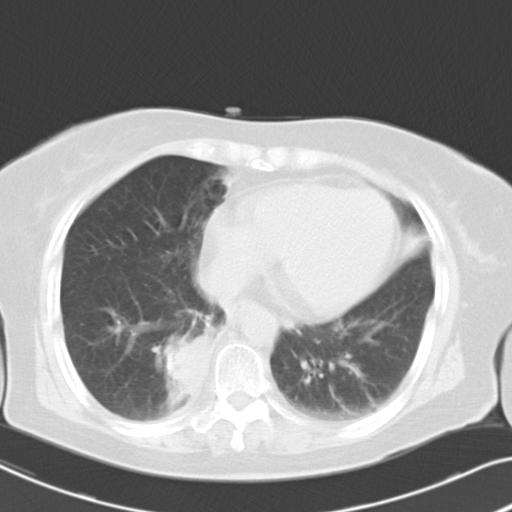
Chest CT, one axial slice; position 9 of 26 along the scan axis; reconstruction kernel B40f; lung window (W 1500 / L -600 HU); 10 mm slice thickness; 512 × 512 image matrix, field of view 333 × 333 mm. Patient: female, 70 years. From the clinical record (not read from this slice): clinical TNM (as recorded): T2 N1 M1a.
Annotated regions visible in this slice (rectangle marked by the reading radiologist):
- lung tumour (recorded histology: adenocarcinoma): bounding box [x1, y1, x2, y2] px = [156, 333, 211, 403]